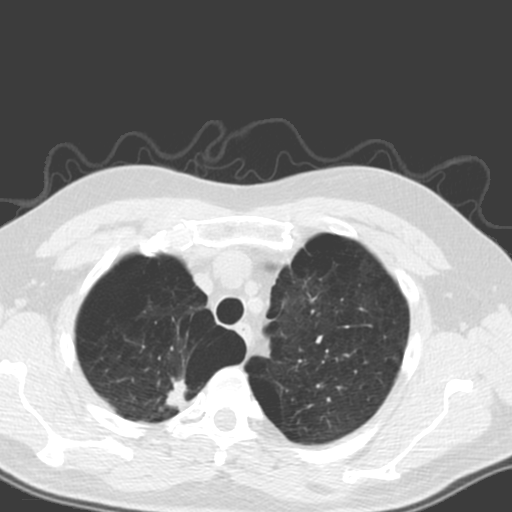
Low-dose screening chest CT, axial slice, first (baseline) screen, lung window (W 1500 / L -600 HU), 3.2 mm slice thickness, standard (soft-tissue) reconstruction kernel (B). Male, age 56 years at enrolment. Former smoker at enrolment.
Lesion marked by an expert reader, bounding box (x1, y1, x2, y2) in pixels: (139, 354, 208, 429). The exam's reader record, not a measurement of the box and not confirmed to be the same lesion: non-calcified nodule or mass ≥4 mm, right upper lobe, 20 × 12 mm, spiculated (stellate) margins, soft tissue attenuation. Official screen result: positive, change unspecified: nodule(s) >= 4 mm or enlarging nodule(s), mass(es), or other non-specific abnormalities suspicious for lung cancer. Participant outcome: lung cancer diagnosed 205 days after this screen — large cell carcinoma, NOS, right upper lobe, poorly differentiated (G3), stage IA (AJCC 6th edition), 18 mm at pathology.